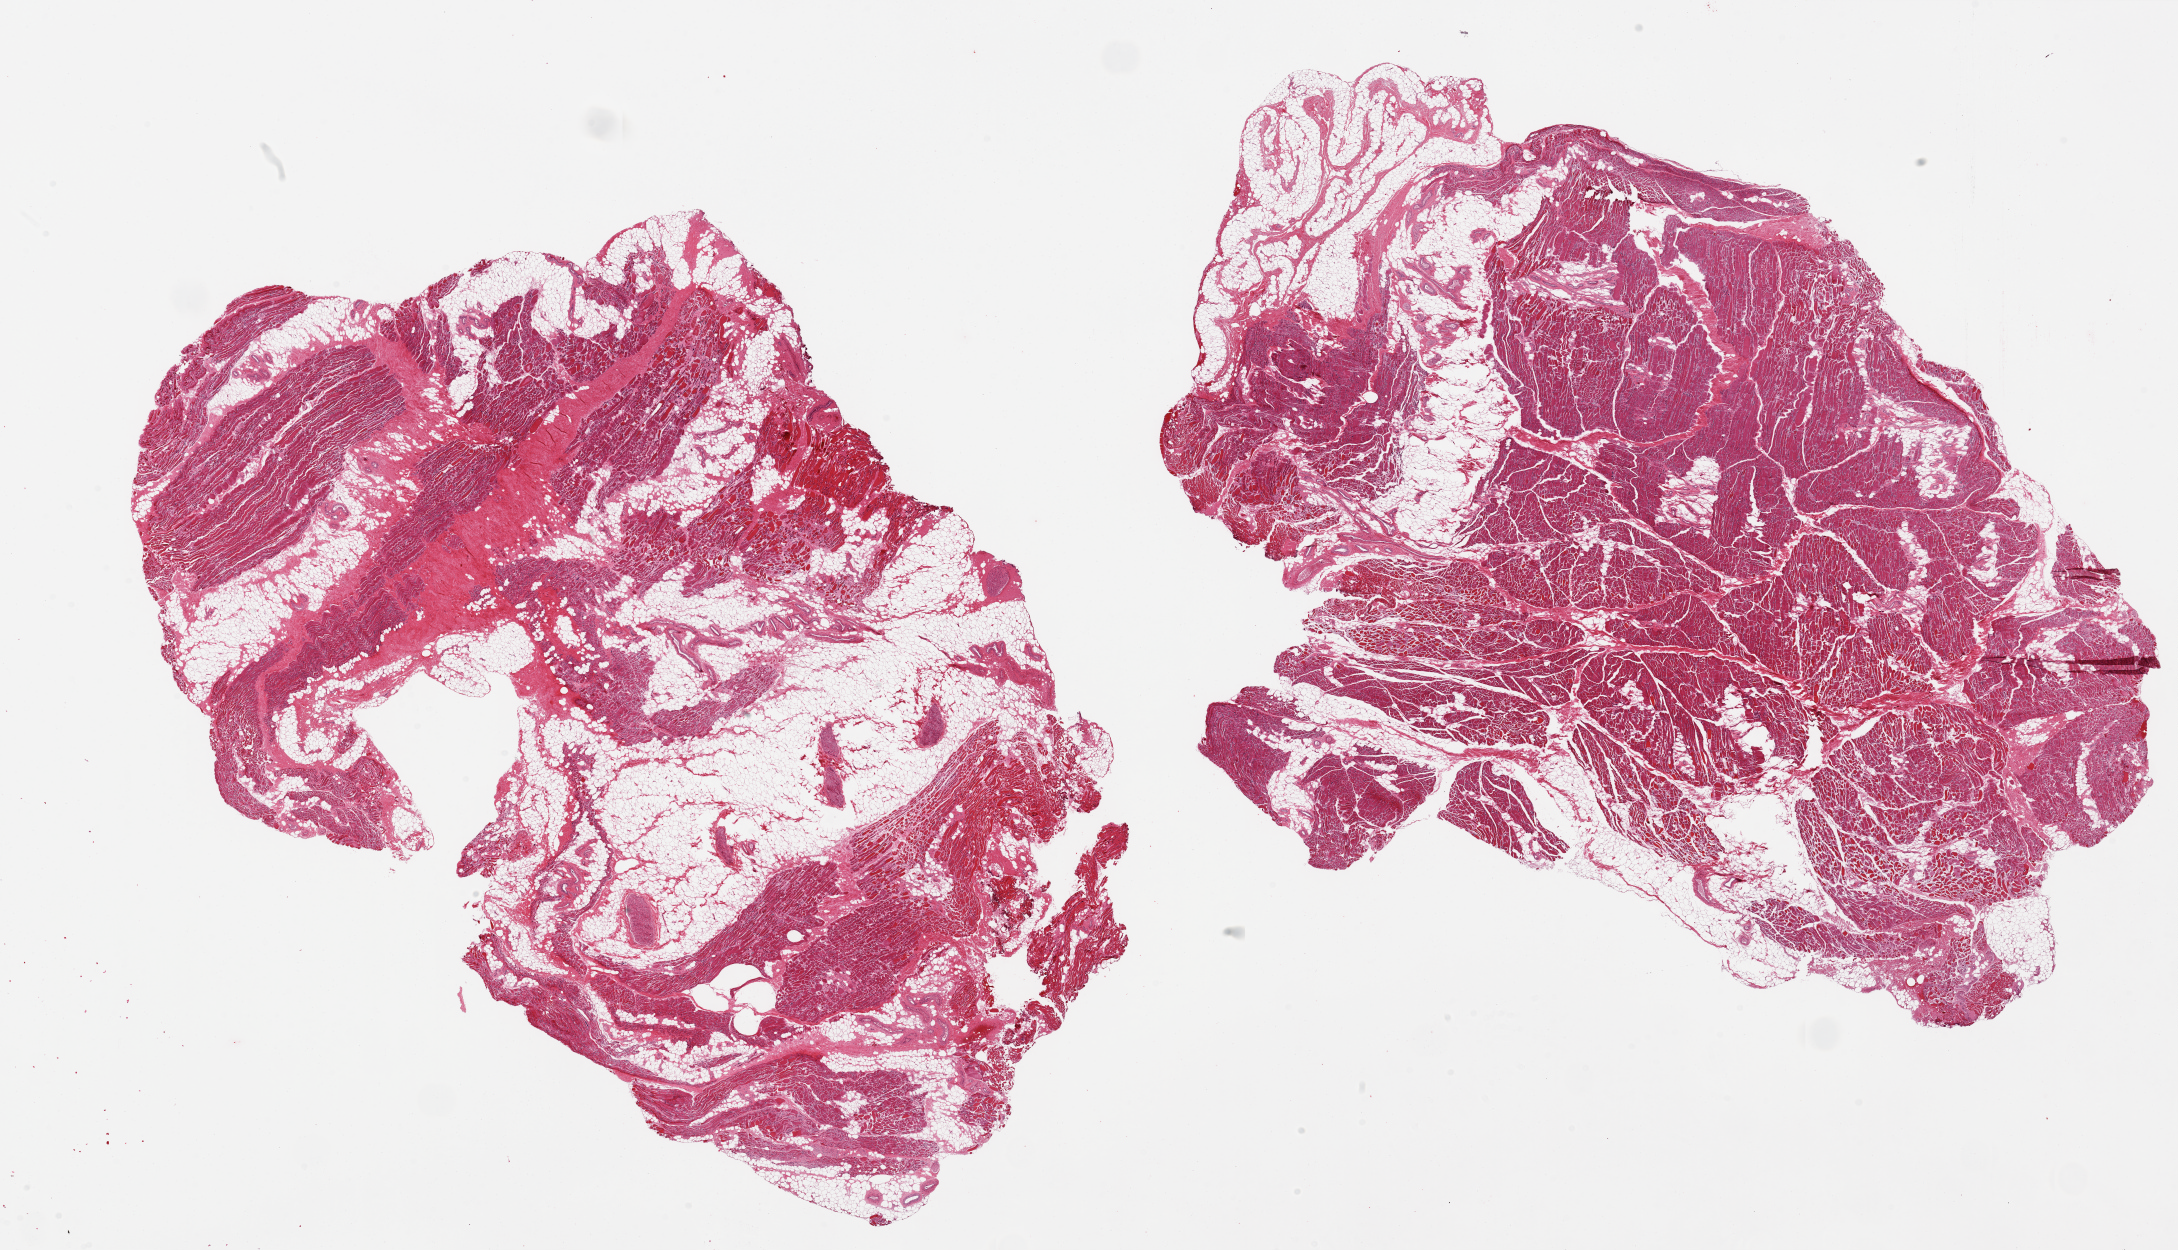
Haematoxylin and eosin whole-slide image, a low-resolution overview of the entire scanned area, about 34.5 x 19.8 mm; PAXgene-fixed paraffin-embedded (PFPE) section; sampled site (target tissue): skeletal muscle; tissue donor sample. Donor: female.
* reviewer comment on this tissue sample: 2 pieces ~17x12mm ; both with internal adipose tissue comprising 20-50% of tissue. Atrophy and interstitial fibrosis